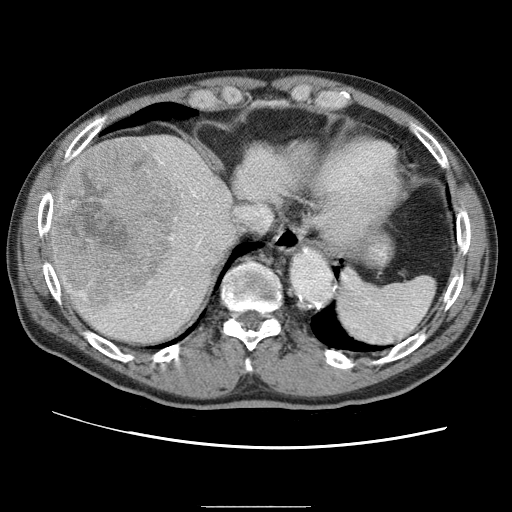
Contrast-enhanced abdominal CT (liver protocol), one axial slice; position 54 of 75 along the scan axis; reconstruction kernel STANDARD; 120 kVp; one of 2 acquisitions stored at this slice position; soft-tissue window (W 400 / L 40 HU); 2.5 mm slice thickness; 512 × 512 image matrix, field of view 360 × 360 mm. Case-level facts recorded for this patient, not image findings: diagnosis: hepatocellular carcinoma (patient treated with transarterial chemoembolisation; whether this scan precedes or follows treatment is not stated here); TNM stage (as recorded): Stage-II; Child-Pugh class: A.
Structures marked on this image (semi-automatic segmentation, software-assisted and operator-edited):
- abdominal aorta: bounding box [x1, y1, x2, y2] px = [291, 250, 332, 305]
- liver parenchyma outside the tumour (the mass and vessels are separate outlines, so this box may not span the whole liver): [50, 134, 313, 346]
- mass: [54, 140, 185, 304]
- liver vessels: [52, 167, 203, 308]